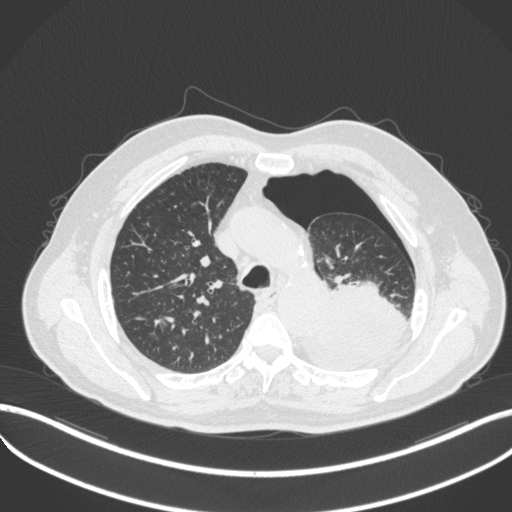
Chest CT, one axial slice; slice 370 of 466 in the series (ordered by position); 120 kVp; lung window (W 1500 / L -600 HU); 1 mm slice thickness; 512 × 512 image matrix. Male patient, age 76 years. Case-level facts recorded for this patient, not image findings: clinical TNM (as recorded): T3 N0 M1b.
Annotated regions visible in this slice (bounding box drawn by a radiologist):
- lung tumour (recorded histology: adenocarcinoma): box from (x=301, y=272) to (x=412, y=365) px